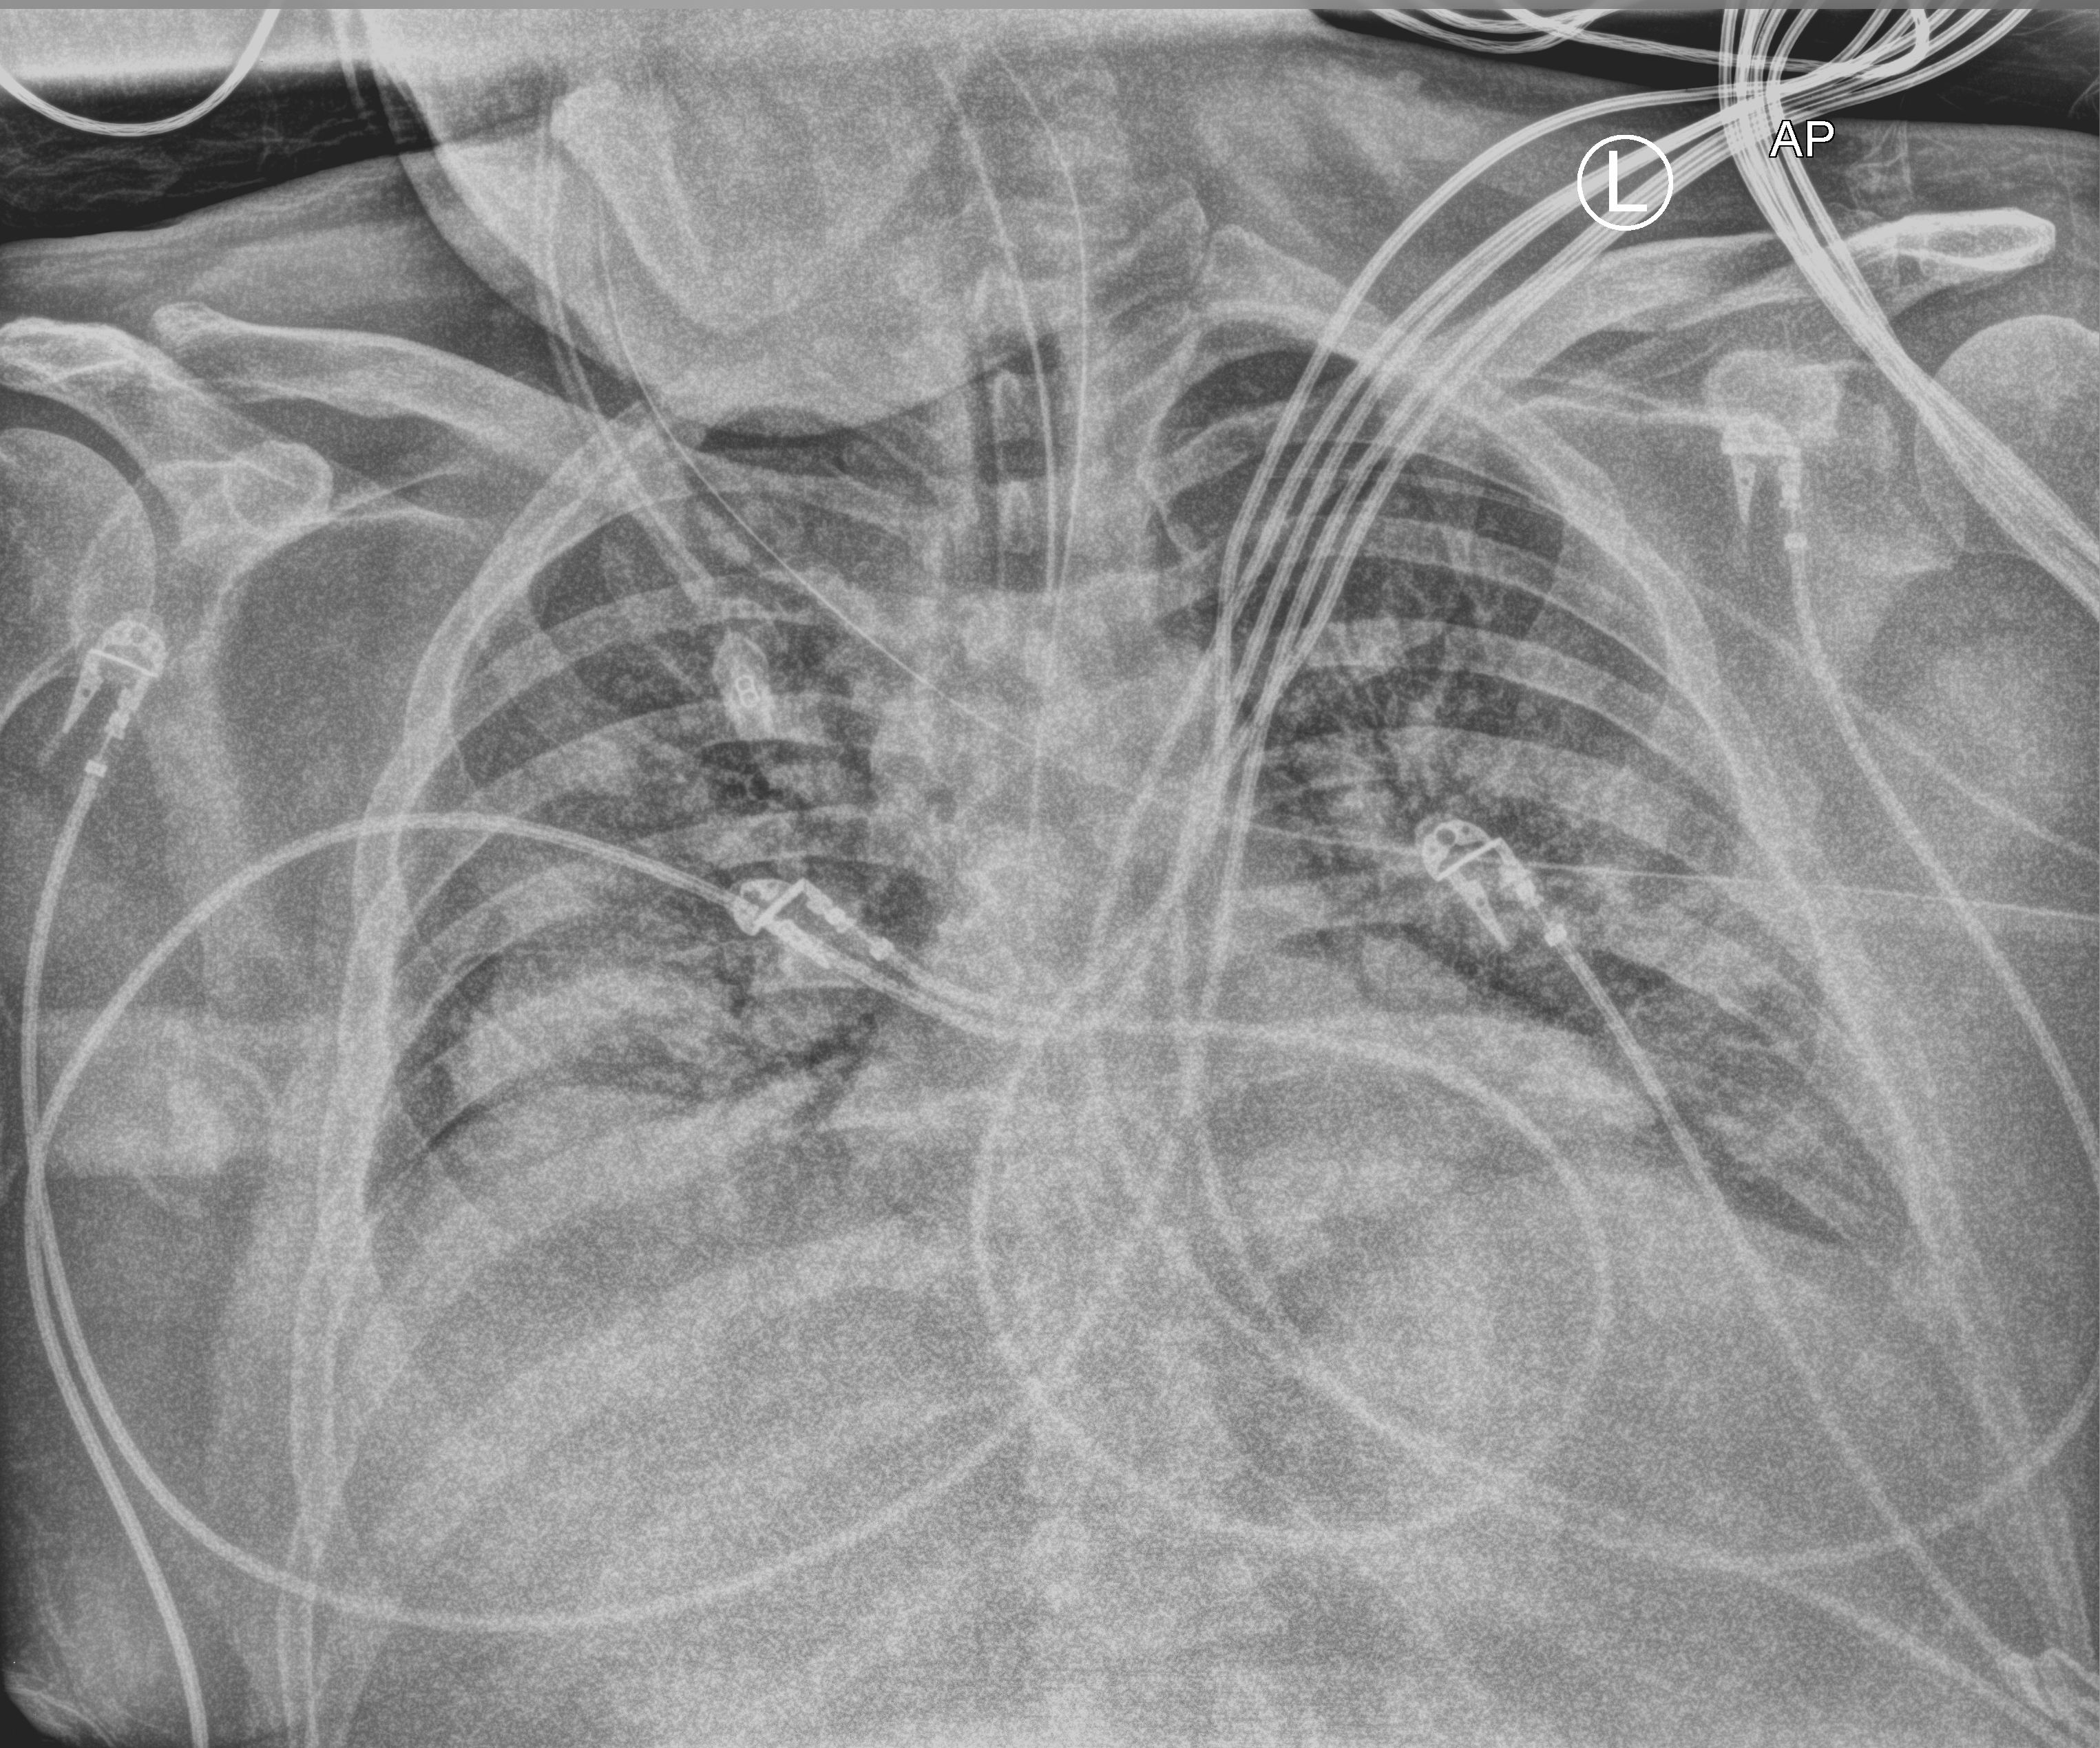
Bedside chest radiograph (computed radiography). Patient hospitalised with COVID-19; male, aged 18–59 years.
Admission-level facts for this patient (not findings on this image; timing relative to this image not recorded): admitted to intensive care during this hospital stay: yes; mechanically ventilated during this hospital stay: yes; length of hospital stay: 80 days.